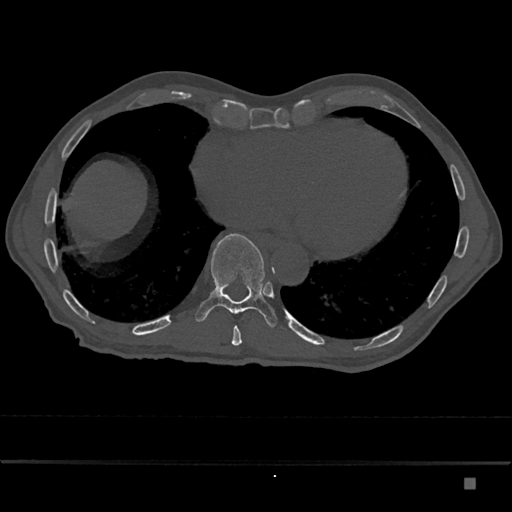
CT including the spine, one axial slice; slice 751 of 797 in the series (ordered by position); 120 kVp; bone window (W 1800 / L 400 HU); 0.5 mm slice thickness; 512 × 512 image matrix. Patient: male, 72 years. From the clinical record (not read from this slice): primary cancer: prostate.
Structures marked on this image (semi-automatic segmentation, software-assisted and operator-edited):
- T10 vertebra: bounding box <195,233,278,328> (left, top, right, bottom; pixels)
- T9 vertebra: <231,326,242,346>